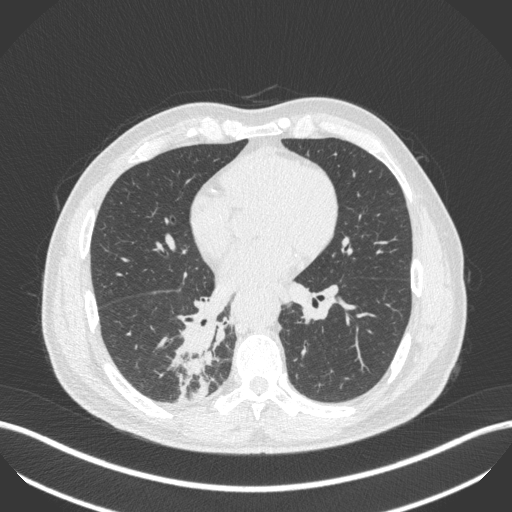
Chest CT, one axial slice; position 215 of 451 along the scan axis; reconstruction kernel B31f; 100 kVp; lung window (W 1500 / L -600 HU); 1 mm slice thickness; 512 × 512 image matrix, field of view 400 × 400 mm. Male patient, age 61 years. From the clinical record (not read from this slice): clinical TNM (as recorded): T1 N0 M0.
Annotated regions visible in this slice (rectangle marked by the reading radiologist):
- lung tumour (recorded histology: small cell carcinoma): box from (x=179, y=320) to (x=219, y=395) px